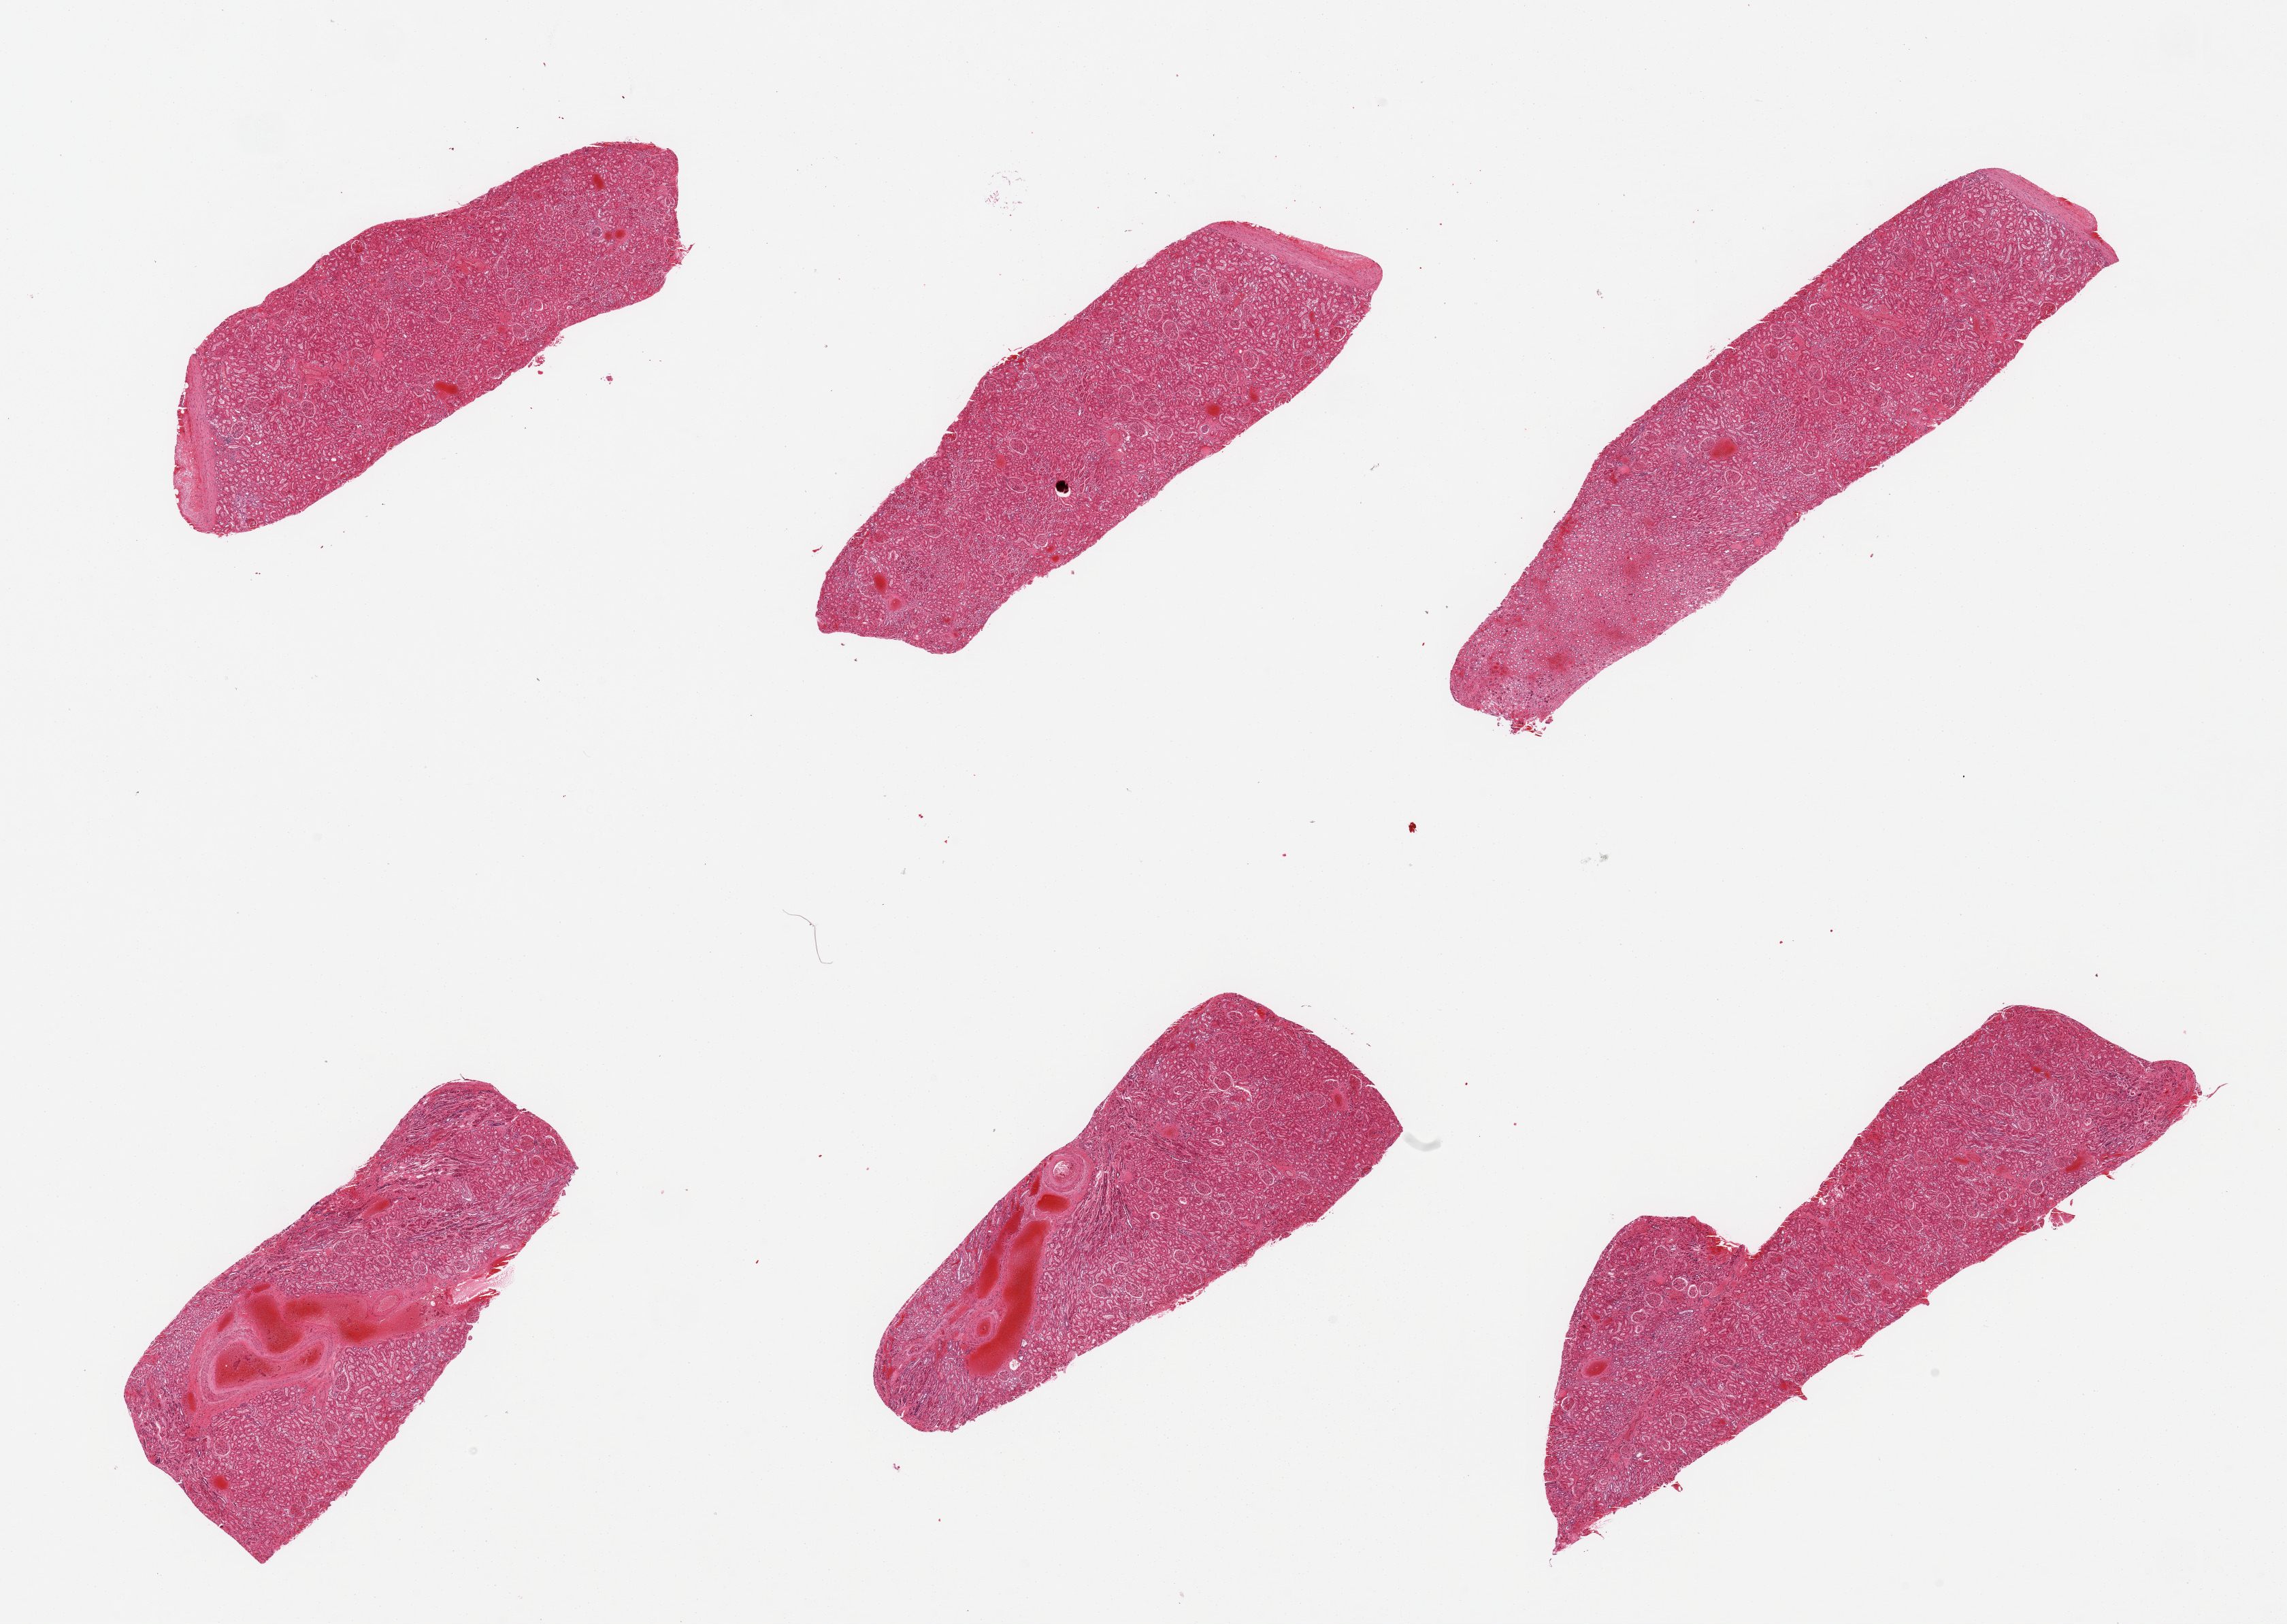
H&E whole-slide image, shown as a low-resolution overview of the whole scanned area (about 26.6 x 18.9 mm). PAXgene-fixed, paraffin-embedded tissue. Sampled site (target tissue): renal cortex. Tissue donor sample. Donor sex: male.
- review note (as recorded): 6 pieces, all cortex; glomeruli present